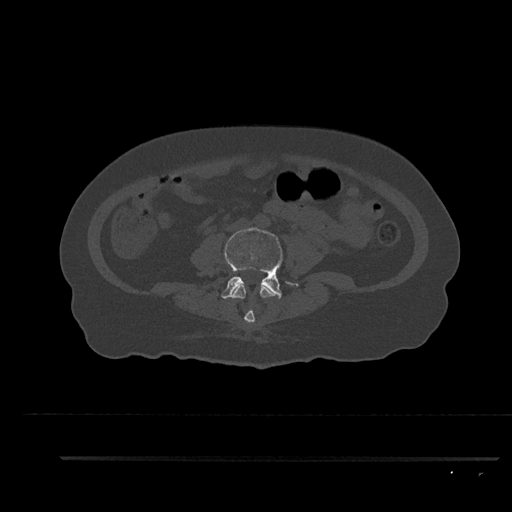
CT including the spine, one axial slice. Slice 43 of 797 in the series (ordered by position). Reconstruction kernel Br40s/3. Bone window (W 1800 / L 400 HU). 0.5 mm slice thickness. 512 × 512 image matrix, field of view 408 × 408 mm. Female patient, age 44 years. From the clinical record (not read from this slice): primary cancer: renal; vertebrae with lytic lesions (as recorded): L1.
Structures marked on this image (semi-automatic segmentation, software-assisted and operator-edited):
- L3 vertebra: bounding box <232,285,281,323> (left, top, right, bottom; pixels)
- L4 vertebra: <221,228,299,299>